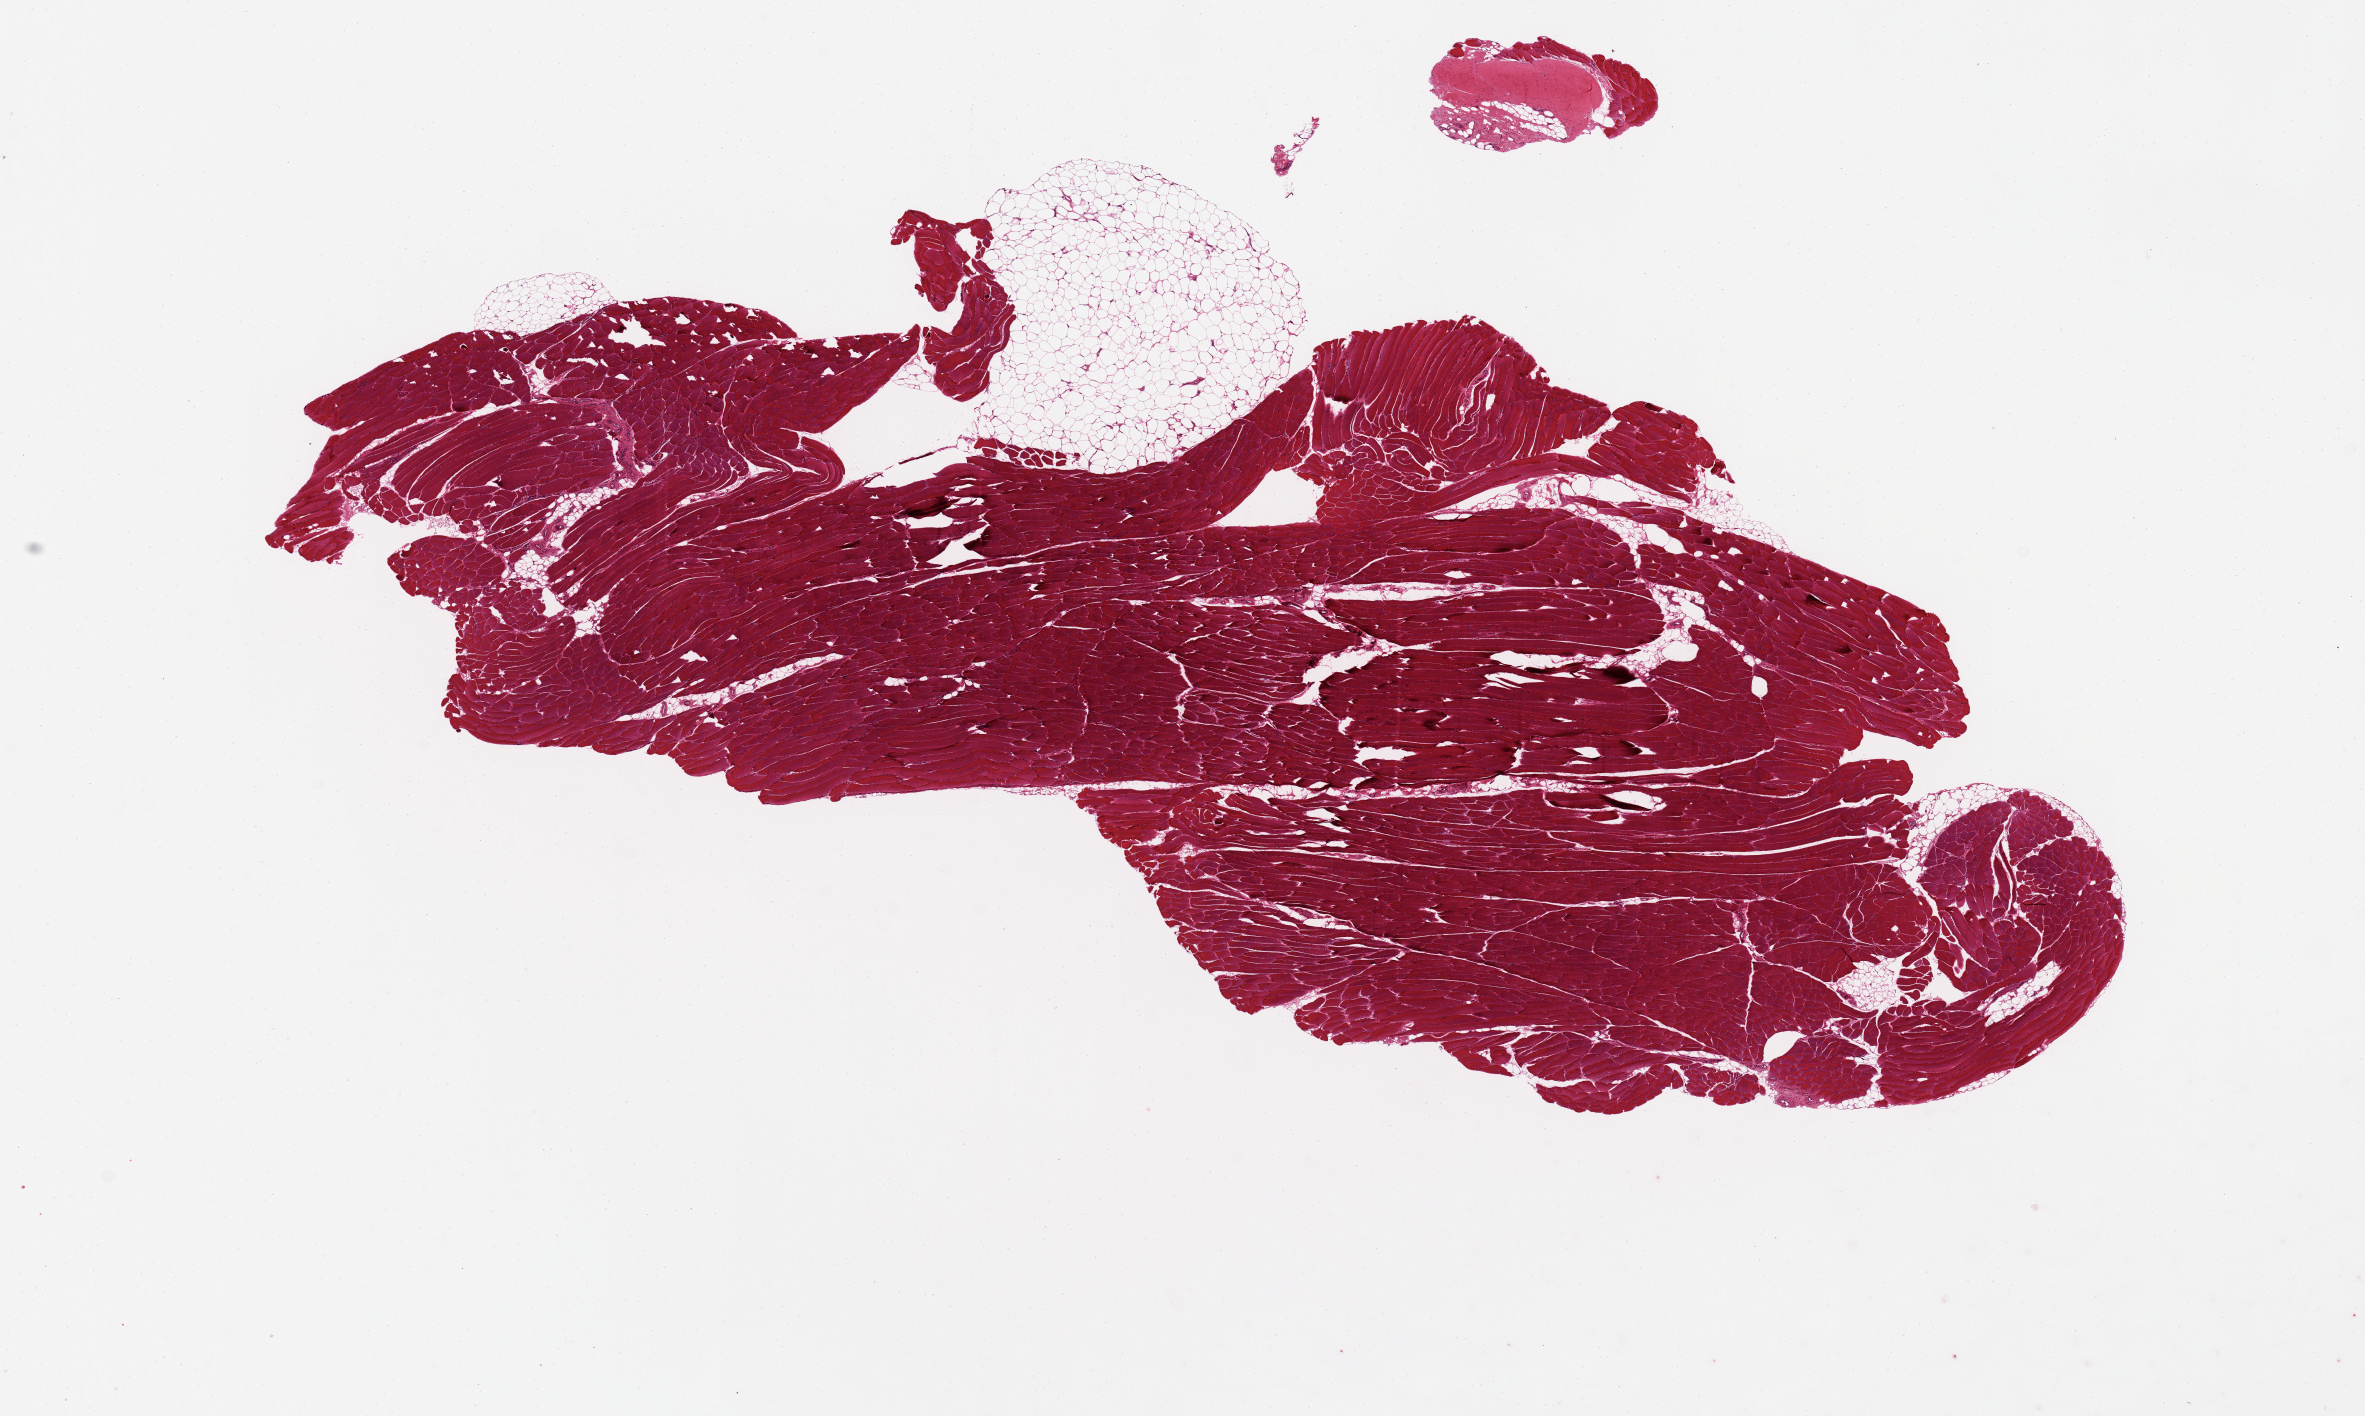
Haematoxylin and eosin whole-slide image, brightfield, a low-resolution overview of the entire scanned area, about 18.7 x 11.2 mm (from a 20x scan); PAXgene-fixed paraffin-embedded (PFPE) section; section of skeletal muscle (target tissue); tissue donor sample. Male donor.
- pathologist's review note for this sample: Approximately 15 x 5mm, good specimen